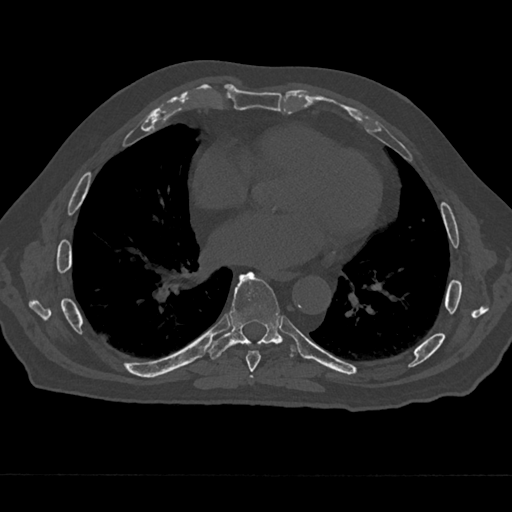
CT including the spine, one axial slice. 120 kVp. Bone window (W 1800 / L 400 HU). 512 × 512 image matrix, field of view 377 × 377 mm. Male patient, age 75 years. From the clinical record (not read from this slice): primary cancer: renal.
Outlined on this slice (semi-automatically segmented with operator editing):
- T6 vertebra: bounding box [x1, y1, x2, y2] px = [250, 375, 253, 379]
- T7 vertebra: [245, 350, 261, 376]
- T8 vertebra: [207, 272, 298, 359]